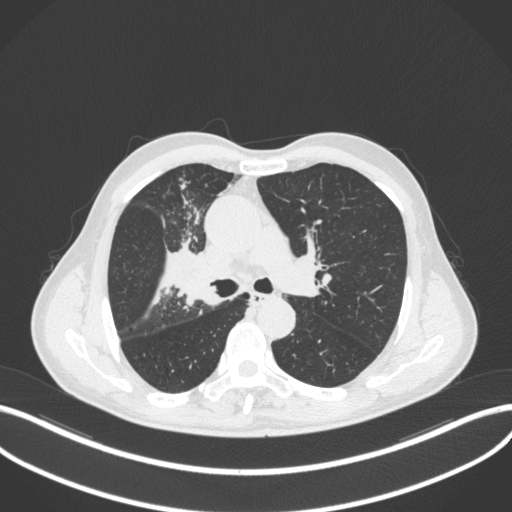
Chest CT, one axial slice; slice 309 of 490 in the series (ordered by position); reconstruction kernel B31f; 120 kVp; lung window (W 1500 / L -600 HU); 512 × 512 image matrix. Patient: male, 69 years. Case-level facts recorded for this patient, not image findings: clinical TNM (as recorded): T2a N0 M0.
Annotated regions visible in this slice (bounding box drawn by a radiologist):
- lung tumour (recorded histology: adenocarcinoma): bounding box (x1, y1, x2, y2) in pixels: (169, 250, 211, 306)